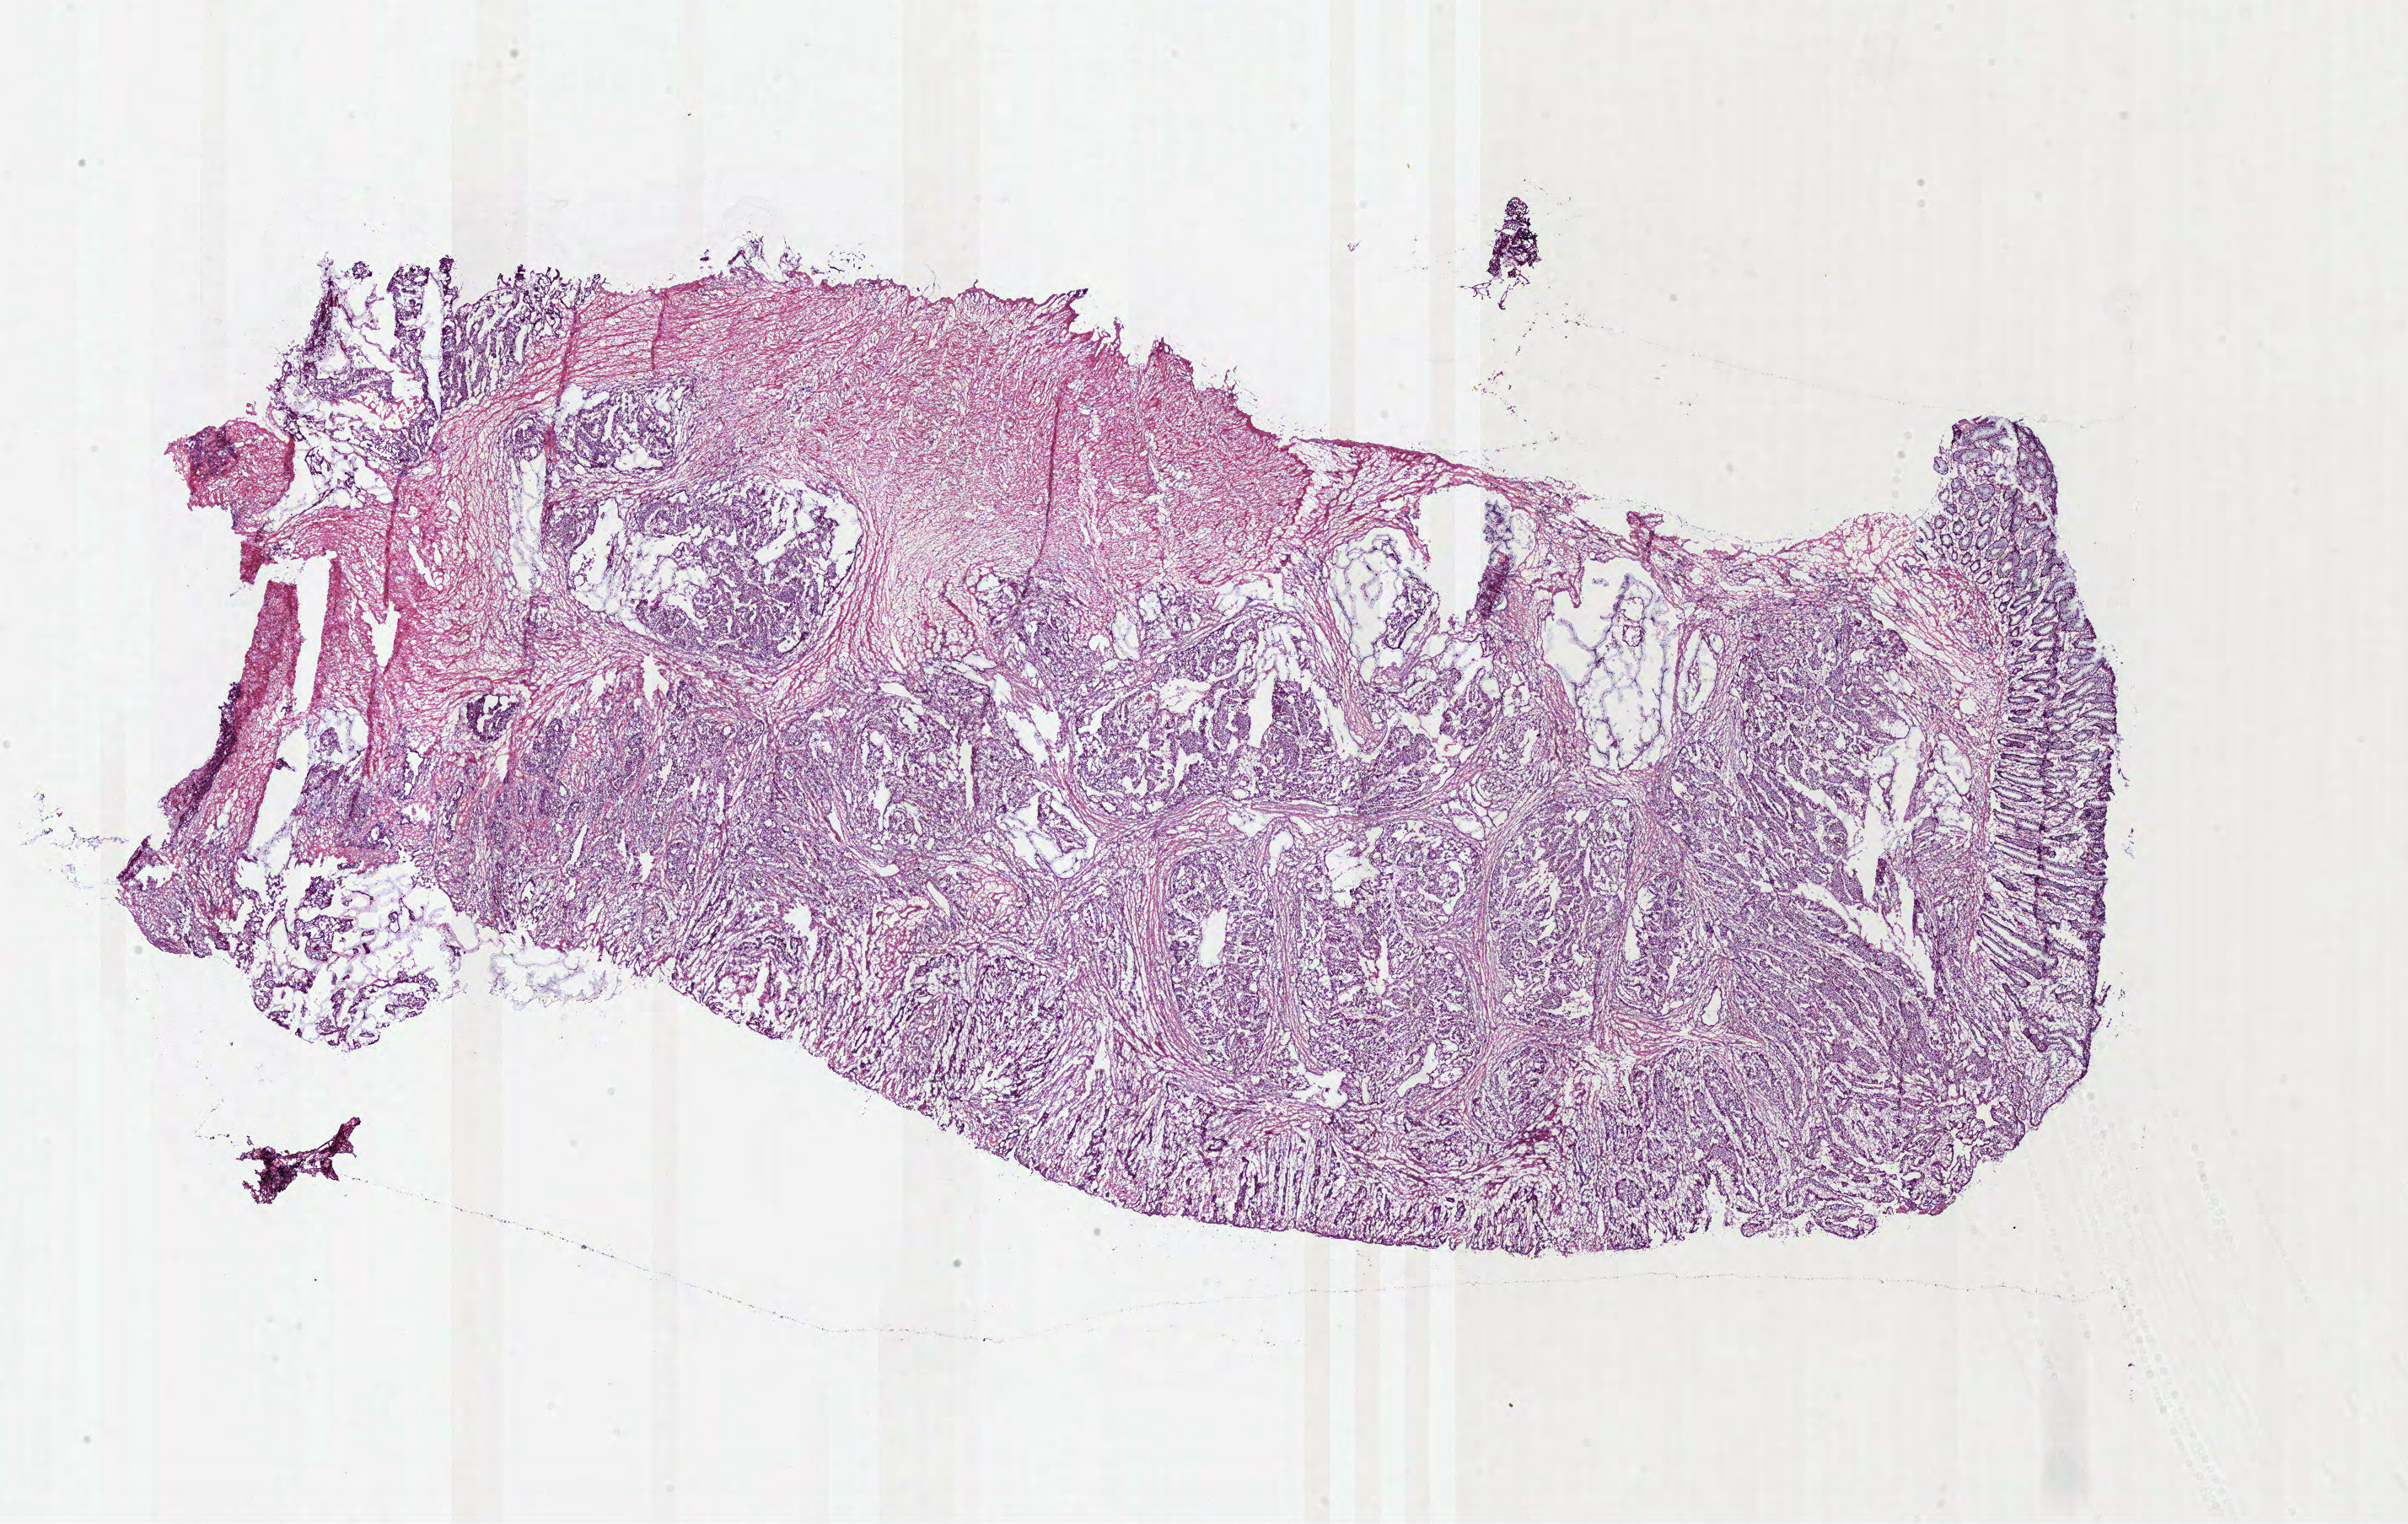
Whole-slide histology image, Hematoxylin and eosin (H&E) stained, whole scanned area (about 22.5 x 14.2 mm, from a 40x scan) shown as a low-resolution overview; frozen section from the bottom of the tissue portion; rectum, primary tumour sample. Patient: female, age at initial diagnosis 60 years. Slide review estimates, as recorded: tumour cells 75%, tumour nuclei 80%, normal cells 5%, stromal cells 20%, necrosis 0%.
• lymph nodes positive (case pathology): 0 of 8 examined
• AJCC pathologic stage: IIA (7th edition)
• pathologic diagnosis: Adenocarcinoma, NOS